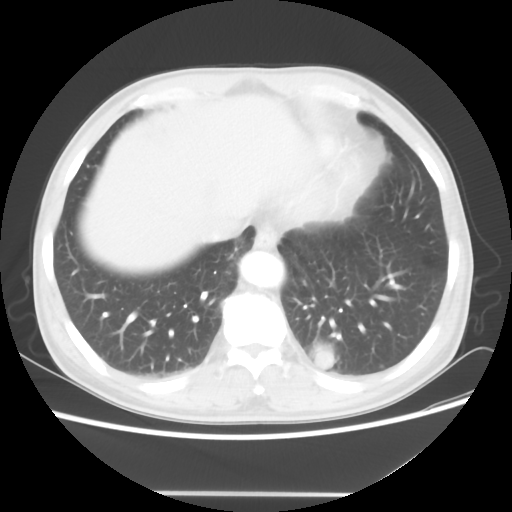
Chest CT, one axial slice; slice 14 of 60 in the series (ordered by position); lung window (W 1500 / L -600 HU); 5 mm slice thickness; 512 × 512 image matrix. Patient: male, 55 years. From the clinical record (not read from this slice): clinical TNM (as recorded): T1c N3 M0; histopathological grade: G3.
Annotated regions visible in this slice (rectangle marked by the reading radiologist):
- lung tumour (recorded histology: small cell carcinoma): bounding box <309,343,343,376> (left, top, right, bottom; pixels)